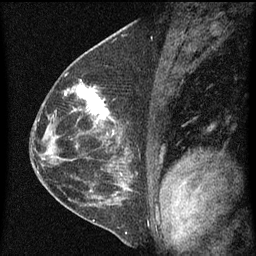
Breast MRI (dynamic contrast-enhanced), one sagittal slice; slice 32 of 60 in the series (ordered by position); dynamic contrast-enhanced series, image 2 of 4 at this slice position (ordered by acquisition); 1.5 T; TE 4.2 ms, TR 8 ms; 2 mm slice thickness; 256 × 256 image matrix, field of view 180 × 180 mm. Female patient, age 48 years.
Structures marked on this image (semi-automatically segmented with operator editing):
- analysis volume of interest (the breast-tissue region the enhancement analysis was run in; not a lesion): box from (x=73, y=82) to (x=115, y=139) px
- tumour enhancement mask (voxels above the 70 % enhancement threshold inside the analysis volume of interest): (x=77, y=82)–(x=114, y=135)